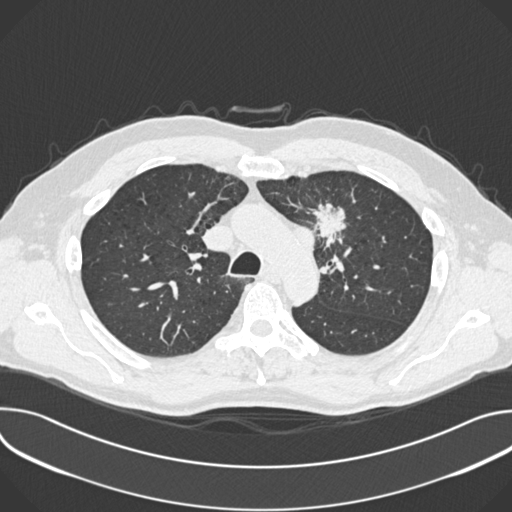
Low-dose screening chest CT, one axial slice. Position 266 of 361 along the scan axis. Reconstruction kernel B30f. 120 kVp. Lung window (W 1500 / L -600 HU). 1 mm slice thickness. 512 × 512 image matrix, field of view 380 × 380 mm.
Annotated regions visible in this slice (expert manual segmentation):
- lesion 1 (tumor, upper lobe of left lung): box from (x=314, y=207) to (x=345, y=245) px